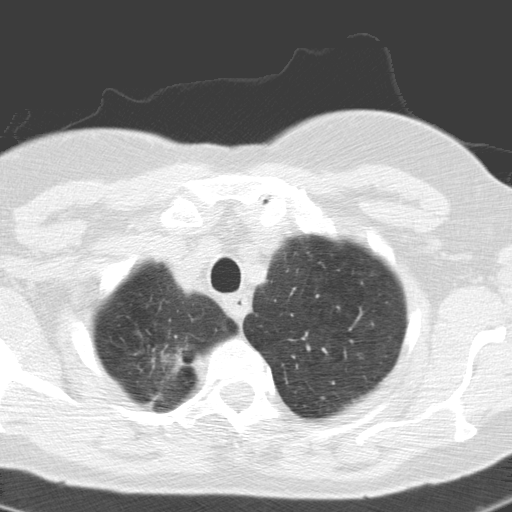
Axial slice from a low-dose chest CT screening exam, first (baseline) screen, lung window (W 1500 / L -600 HU), 3.2 mm slice thickness, standard (soft-tissue) reconstruction kernel (C), slice 15 of 155 in the series, 512 × 512 image matrix. Female participant, aged 60 years at enrolment. Current smoker at enrolment.
Expert reader's lesion annotation, bounding box (x1, y1, x2, y2) in pixels: (119, 333, 197, 407). Screening reader's record for this exam: no non-calcified nodule ≥4 mm recorded. Official screen result: negative screen, minor abnormalities not suspicious for lung cancer. Lung cancer was diagnosed 391 days after this screen: squamous cell carcinoma, keratinizing, NOS, right upper lobe, moderately differentiated (G2), stage IA (AJCC 6th edition), 20 mm at pathology.